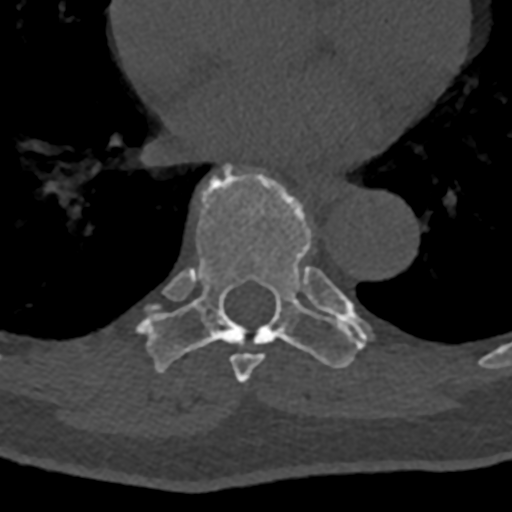
CT including the spine, one axial slice; slice 724 of 797 in the series (ordered by position); reconstruction kernel Br40s/3; 120 kVp; bone window (W 1800 / L 400 HU); 512 × 512 image matrix, field of view 160 × 160 mm. Patient: male, 74 years. Case-level facts recorded for this patient, not image findings: primary cancer: renal.
Annotated regions visible in this slice (semi-automatic segmentation, software-assisted and operator-edited):
- T7 vertebra: box from (x=222, y=172) to (x=347, y=383) px
- T8 vertebra: (x=137, y=162)–(x=371, y=372)